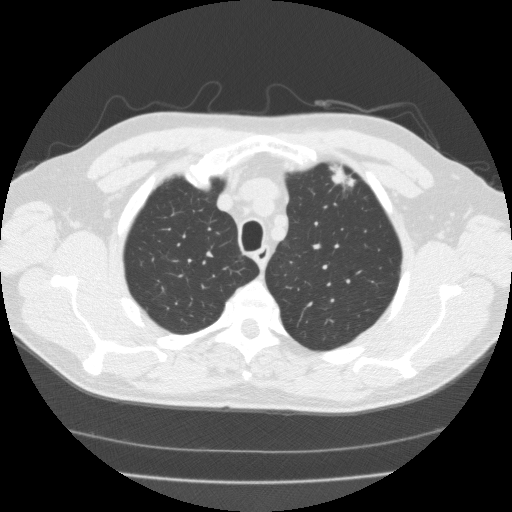
Low-dose screening chest CT, axial slice; third screening round (two years after baseline); lung window (W 1500 / L -600 HU); 2 mm slice thickness; 512 × 512 image matrix, field of view 359 × 359 mm. Male participant, aged 56 years at enrolment. Former smoker at enrolment.
• Expert-annotated lung lesion, box from (x=321, y=159) to (x=364, y=196) px.
• The exam's reader record, not a measurement of the box and not confirmed to be the same lesion: non-calcified nodule or mass ≥4 mm, left upper lobe, 18 × 10 mm, spiculated (stellate) margins, soft tissue attenuation, pre-existing on the prior screen: yes; interval growth: yes.
• Official screen result: positive, other.
• Participant outcome: lung cancer diagnosed 119 days after this screen — adenocarcinoma, NOS, left upper lobe, moderately differentiated (G2), stage IA (AJCC 6th edition), 15 mm at pathology.